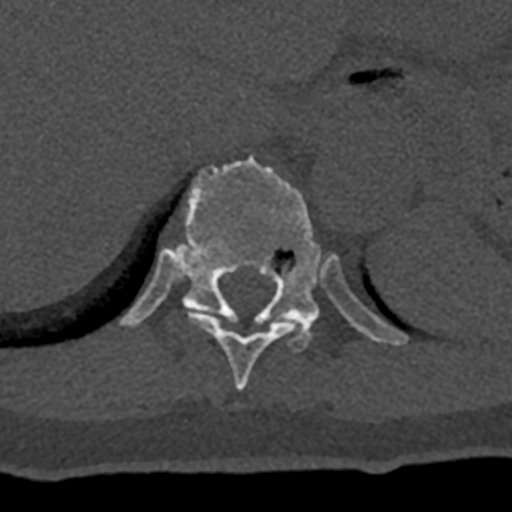
CT including the spine, one axial slice; position 573 of 797 along the scan axis; reconstruction kernel Br40s/3; 120 kVp; bone window (W 1800 / L 400 HU); 0.5 mm slice thickness; 512 × 512 image matrix, field of view 160 × 160 mm. Male patient, age 74 years. Case-level facts recorded for this patient, not image findings: primary cancer: renal.
Structures marked on this image (semi-automatic segmentation, software-assisted and operator-edited):
- T10 vertebra: bounding box <189,313,310,392> (left, top, right, bottom; pixels)
- T11 vertebra: <119,156,408,352>